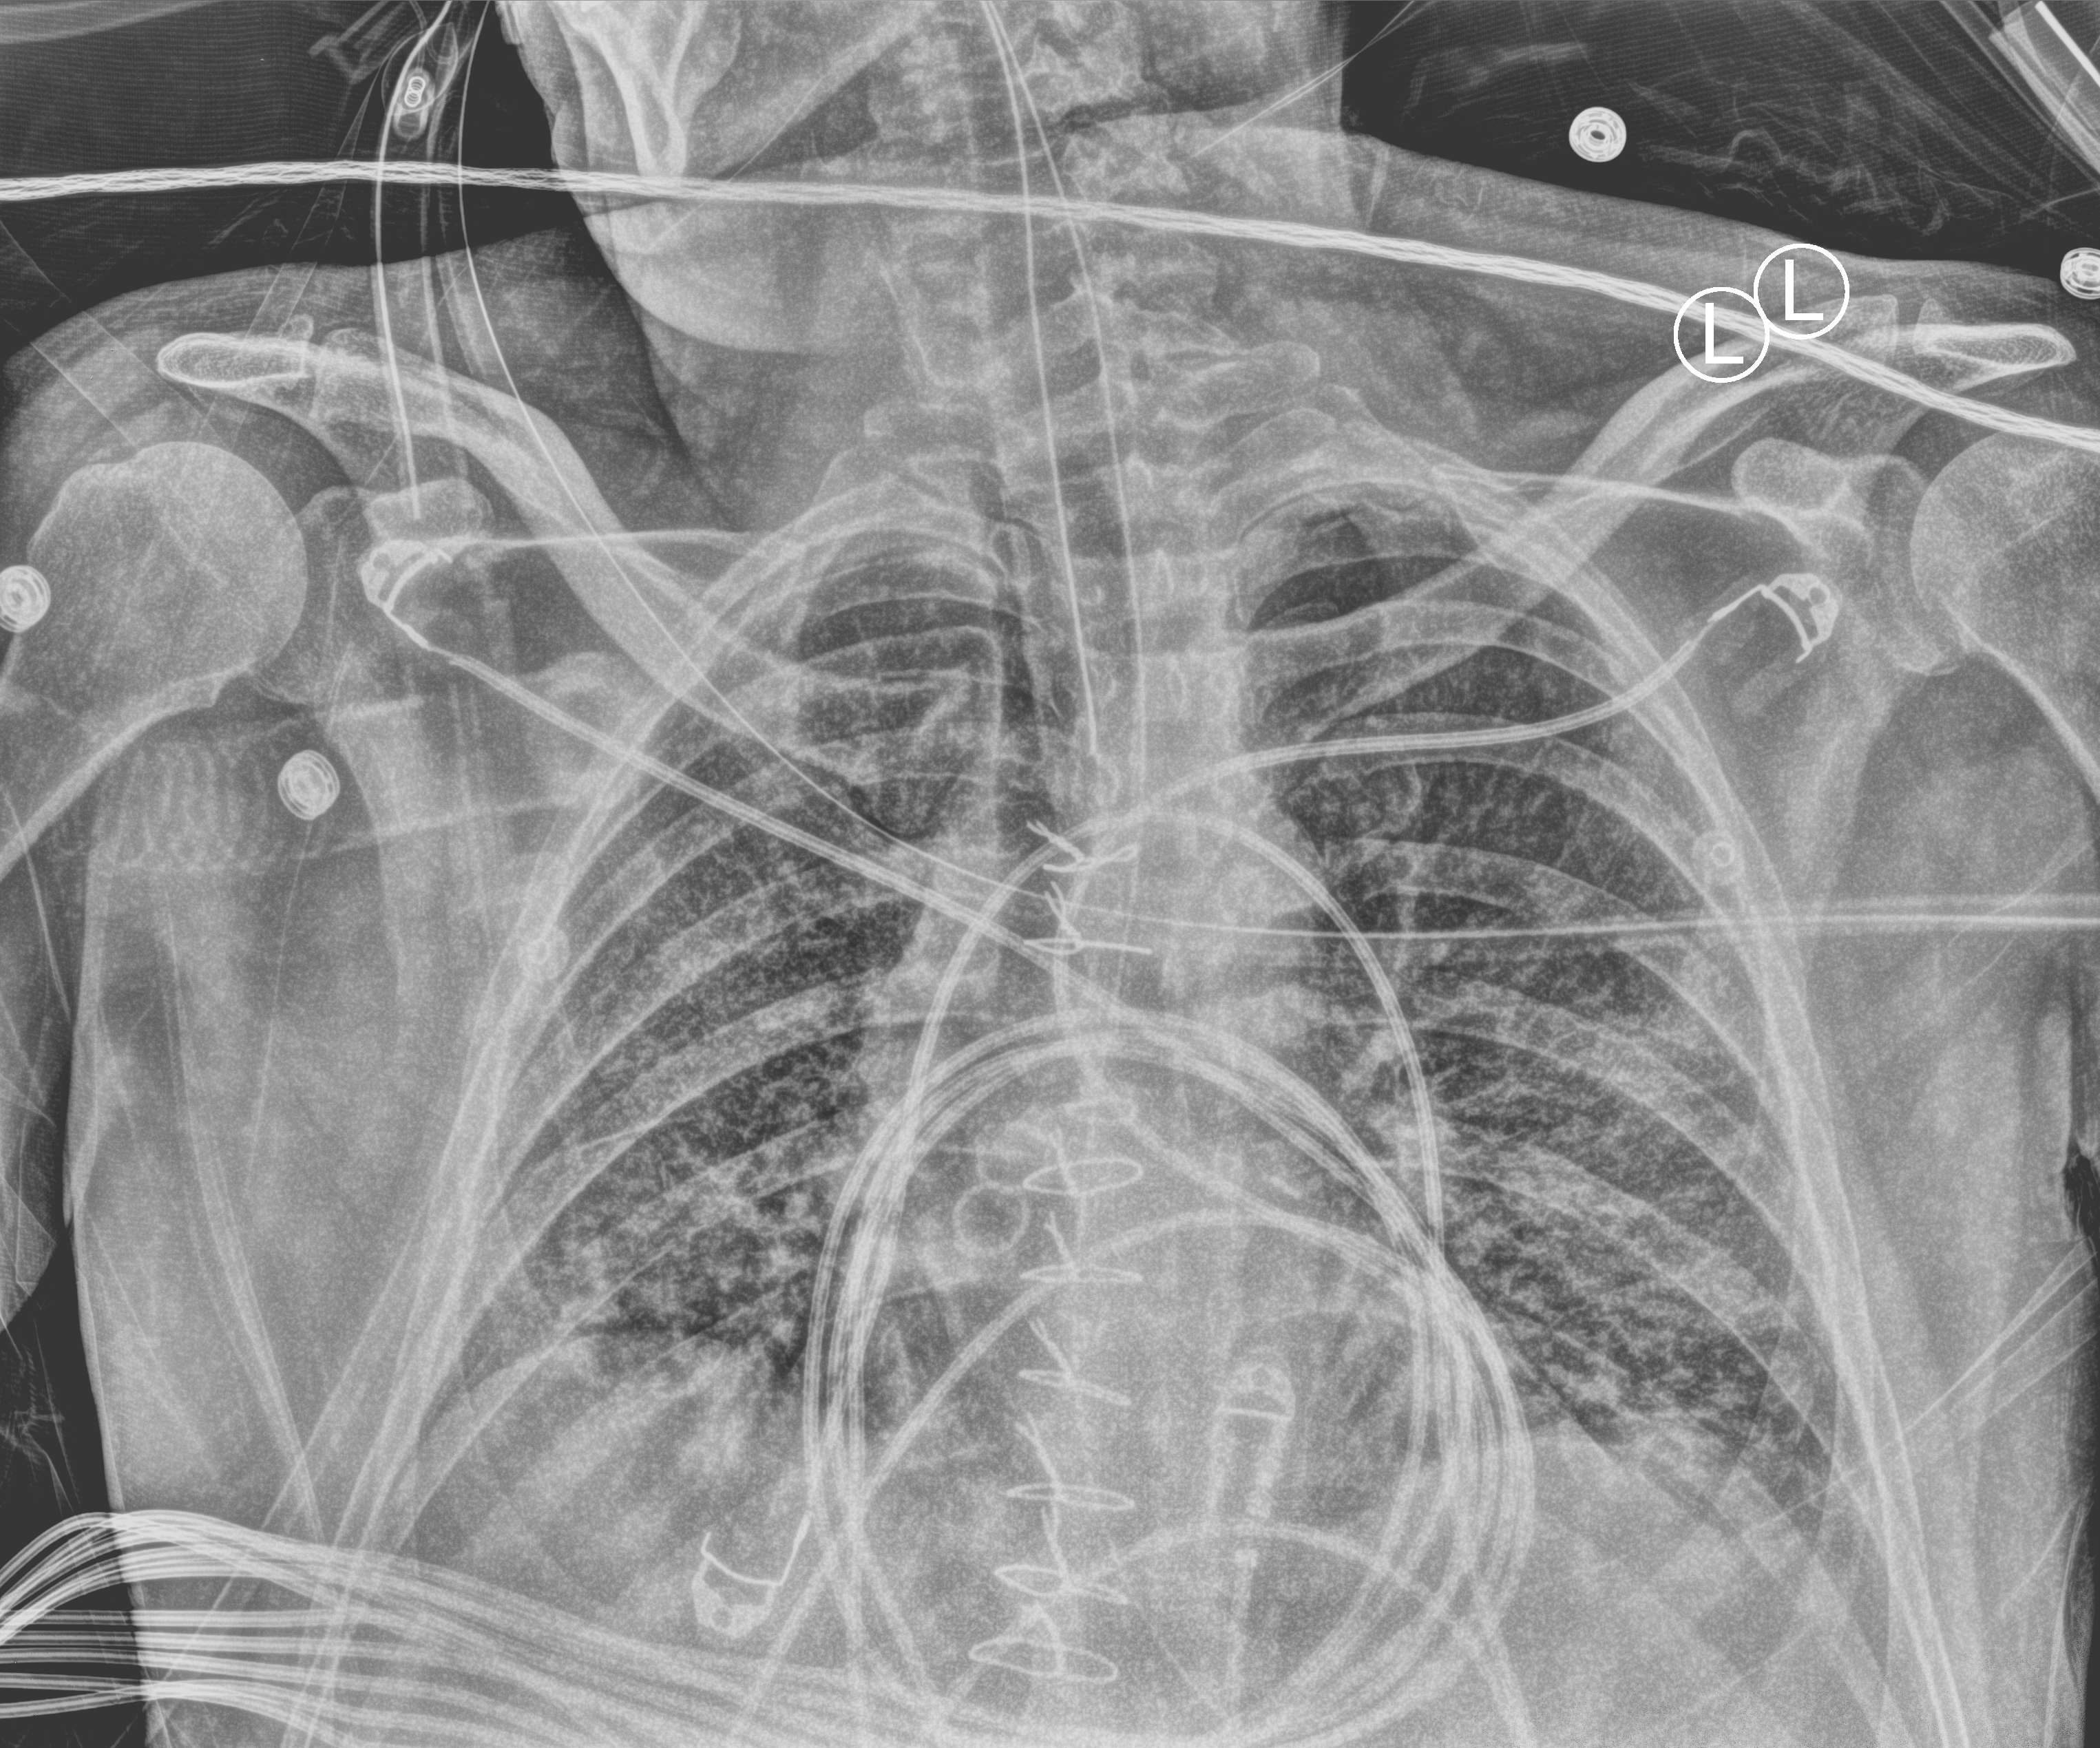
Chest X-ray (portable), anteroposterior (AP) projection. Patient hospitalised with COVID-19; male, aged 18–59 years.
Hospital-stay facts (about this admission, not read from this image; timing relative to this image not recorded): mechanically ventilated during this hospital stay: yes; length of hospital stay: 63 days.